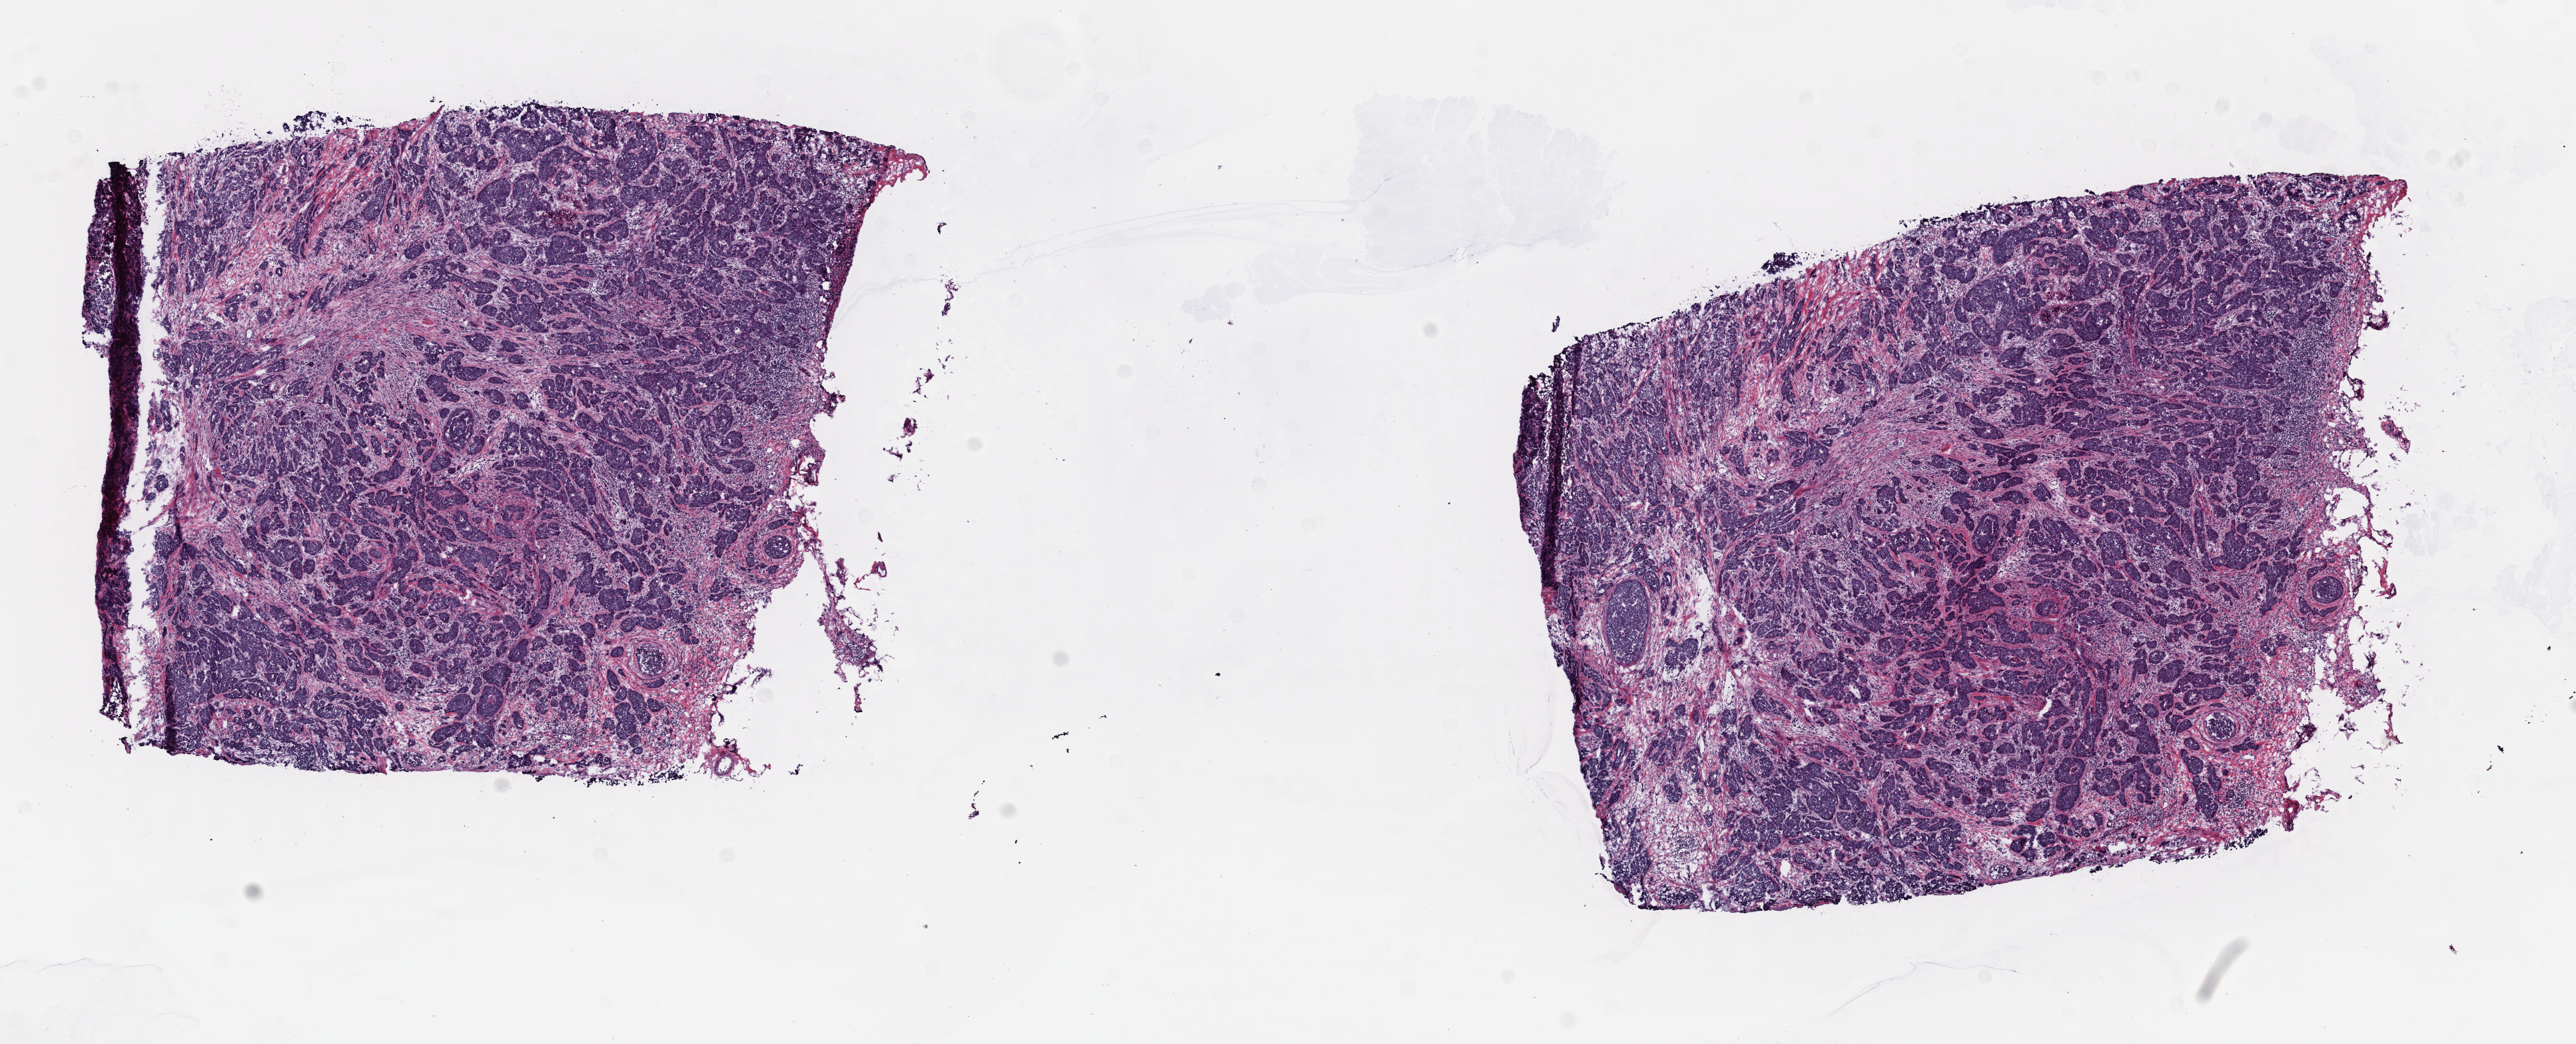
Digitized H&E tissue section (whole slide) — shown as a low-resolution overview of the whole scanned area (about 15.3 x 6.2 mm, from a 40x scan). Frozen section from the top of the tissue portion. Breast, primary tumour sample. Female patient; age at initial diagnosis 81 years. Composition of this section per pathologist review: tumour cells 95%, tumour nuclei 85%, normal cells 0%, stromal cells 5%, necrosis 0%. Inflammatory infiltration, as recorded: lymphocyte infiltration 0%, monocyte infiltration 0%, neutrophil infiltration 0%.
Lymph nodes positive (case pathology): 6 of 14 examined. AJCC pathologic stage: IIIA. Histologic diagnosis: Infiltrating duct carcinoma, NOS. Laterality: right.